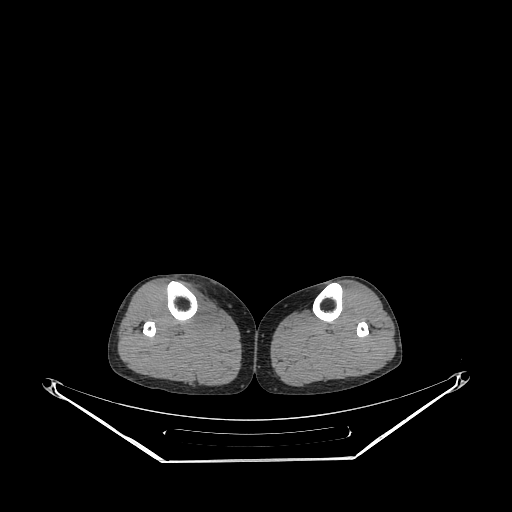
CT of an extremity soft-tissue mass (from a PET/CT study), one axial slice; position 145 of 267 along the scan axis; reconstruction kernel STANDARD; 140 kVp; soft-tissue window (W 400 / L 40 HU); 512 × 512 image matrix. Female patient. From the clinical record (not read from this slice): histological type: undifferentiated – high grade; grade: high; site of the primary tumour: right thigh.
Annotated regions visible in this slice (expert contour drawn on MRI and transferred to this co-registered scan by the dataset authors):
- gross tumour volume (mass): box from (x=185, y=285) to (x=213, y=328) px